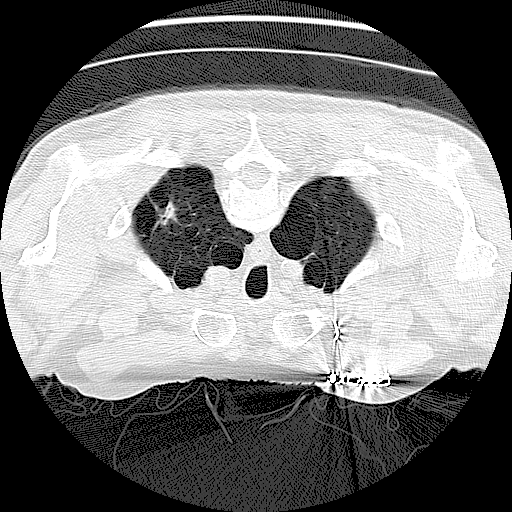
Axial slice from a low-dose chest CT screening exam, baseline screening round, lung window (W 1500 / L -600 HU), slice 19 of 138 in the series, 512 × 512 image matrix, field of view 330 × 330 mm. Male, age 73 years at enrolment.
Expert-annotated lung lesion, bounding box (x1, y1, x2, y2) in pixels: (143, 189, 187, 236). The screening reader recorded 2 non-calcified nodules or masses ≥4 mm on this exam; which of them this box marks is not recorded. Lung cancer was diagnosed 308 days after this screen: neoplasm, malignant, stage IV (AJCC 6th edition).